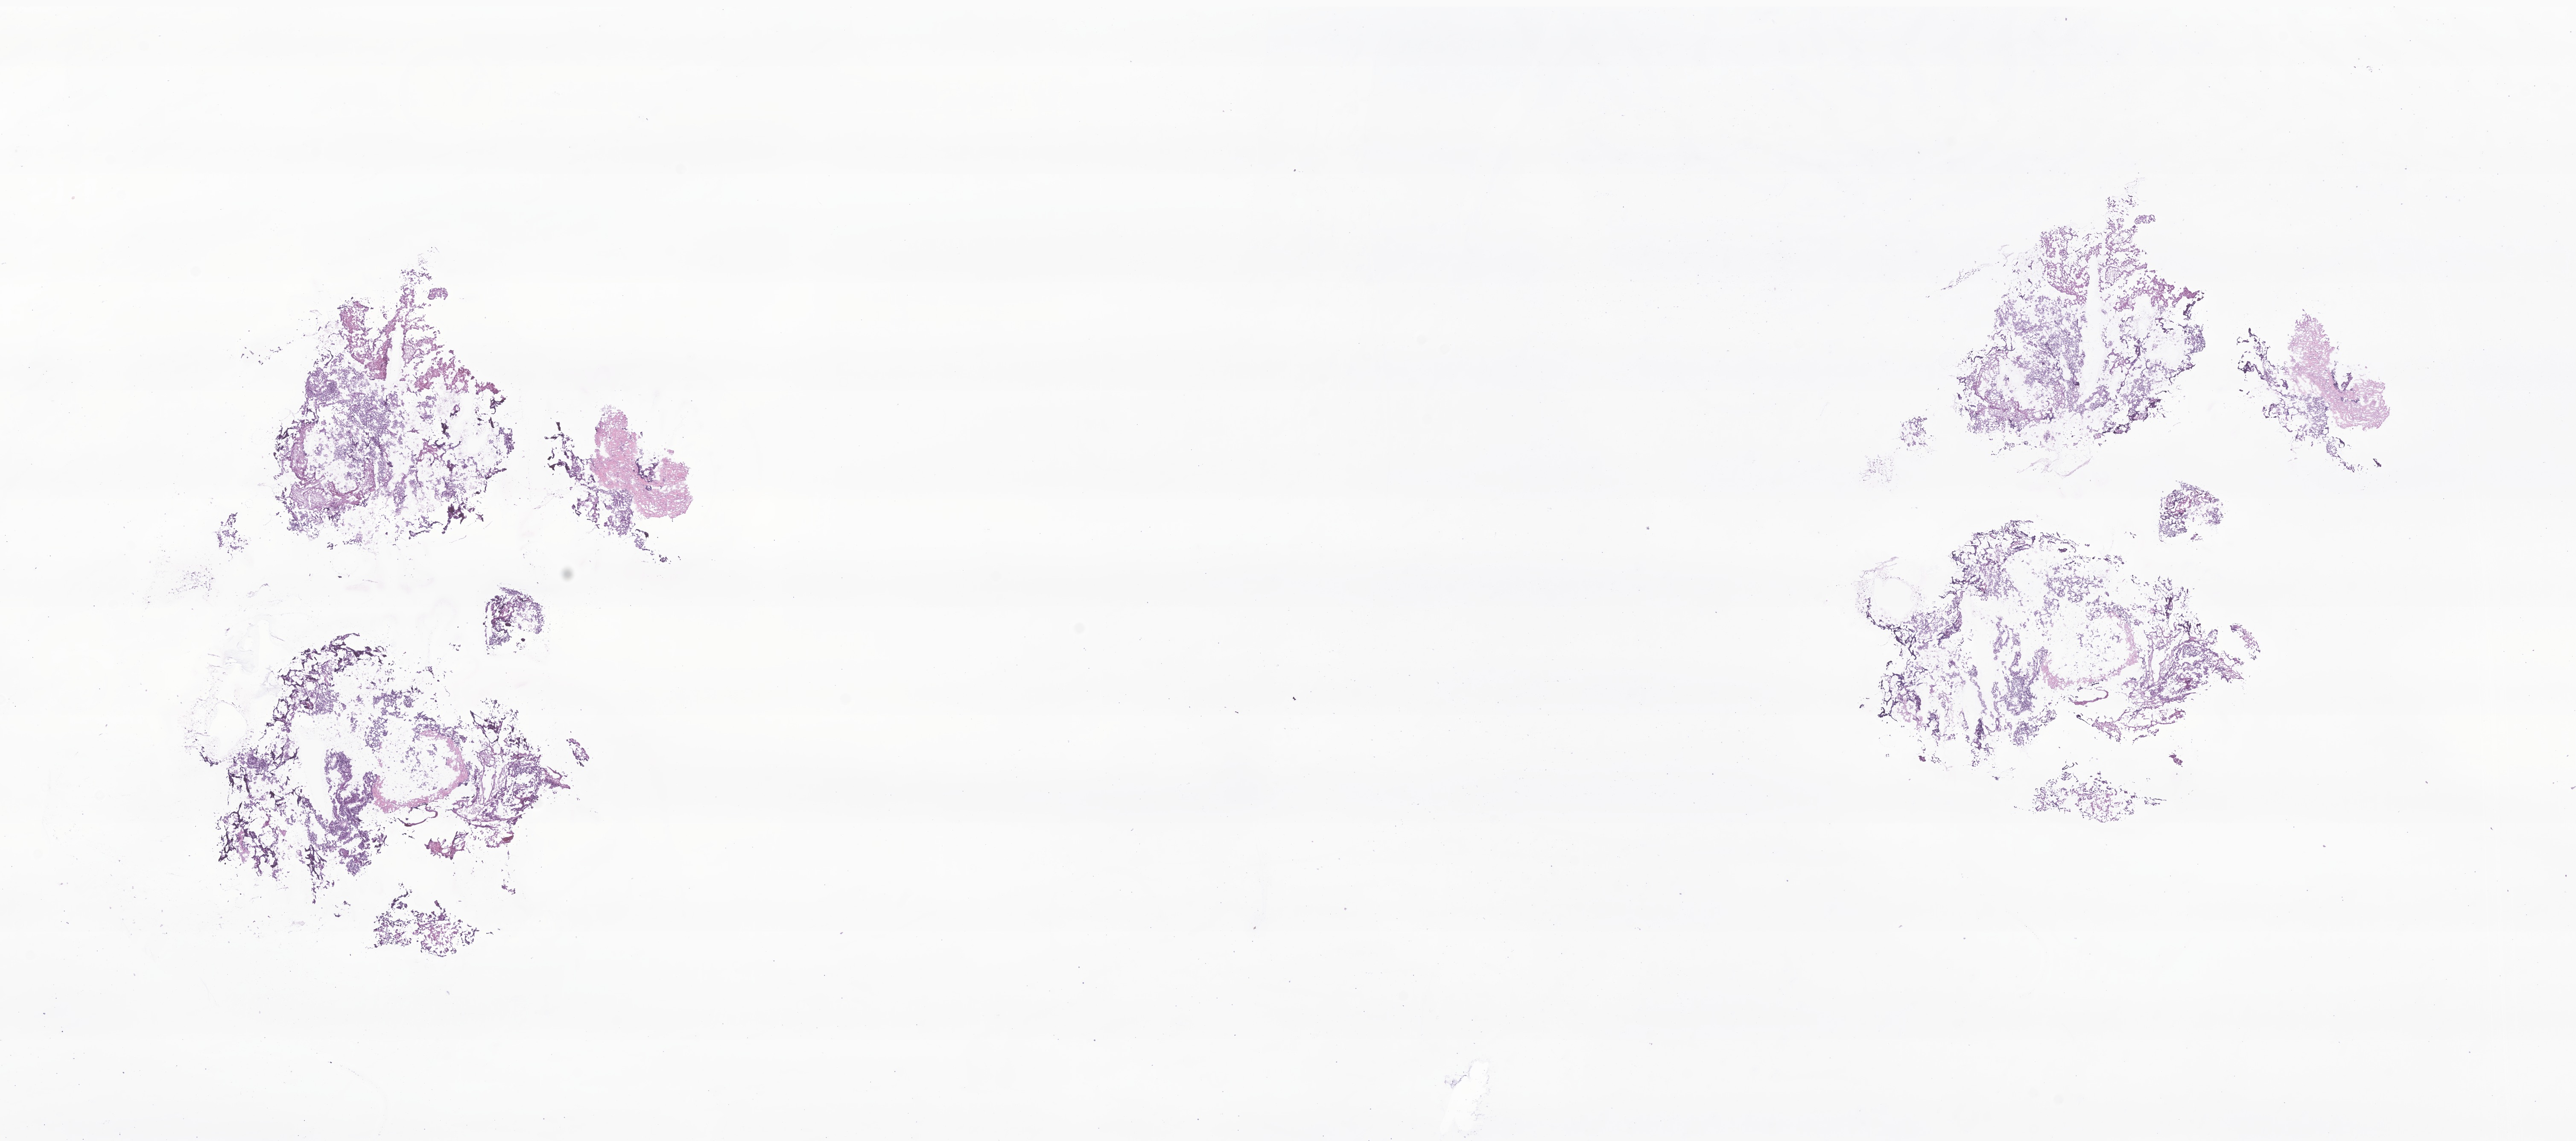
Digitized haematoxylin and eosin-stained section of tumor tissue from the brain, a low-resolution overview of the entire scanned area, about 25.4 x 11.3 mm. Frozen section (OCT-embedded). Patient male; age 862 days (about 2.4 years).
• diagnosis (ICD-O-3 morphology term): Choroid plexus carcinoma